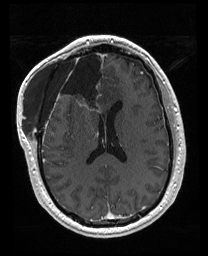
Brain MRI from a brain-tumour surgery series, one axial slice. Position 78 of 176 along the scan axis. T1-weighted post-contrast. 1 mm slice thickness. 208 × 256 image matrix. From the clinical record (not read from this slice): histopathology: Astrocytoma; WHO grade: 4; IDH mutation: yes; tumour location: Right Orbitofrontal Anterior Temporal Insular.
Outlined on this slice (outlined manually by an expert reader):
- previous resection cavity: bounding box <56,52,106,111> (left, top, right, bottom; pixels)